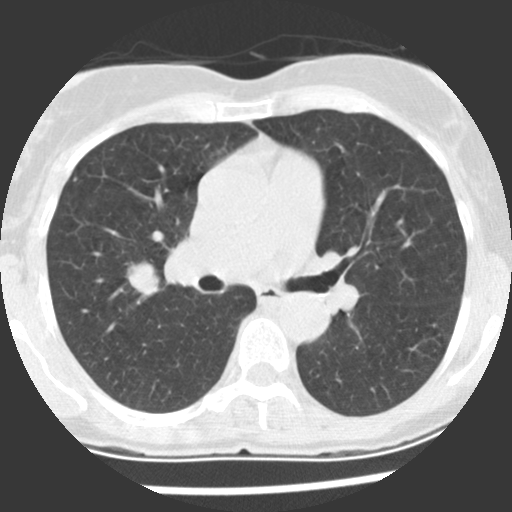
Low-dose screening chest CT, one axial slice. Slice 127 of 225 in the series (ordered by position). Reconstruction kernel STANDARD. Lung window (W 1500 / L -600 HU). 512 × 512 image matrix, field of view 270 × 270 mm.
Outlined on this slice (outlined manually by an expert reader):
- lesion 1 (tumor, upper lobe of right lung): bounding box <127,262,159,297> (left, top, right, bottom; pixels)